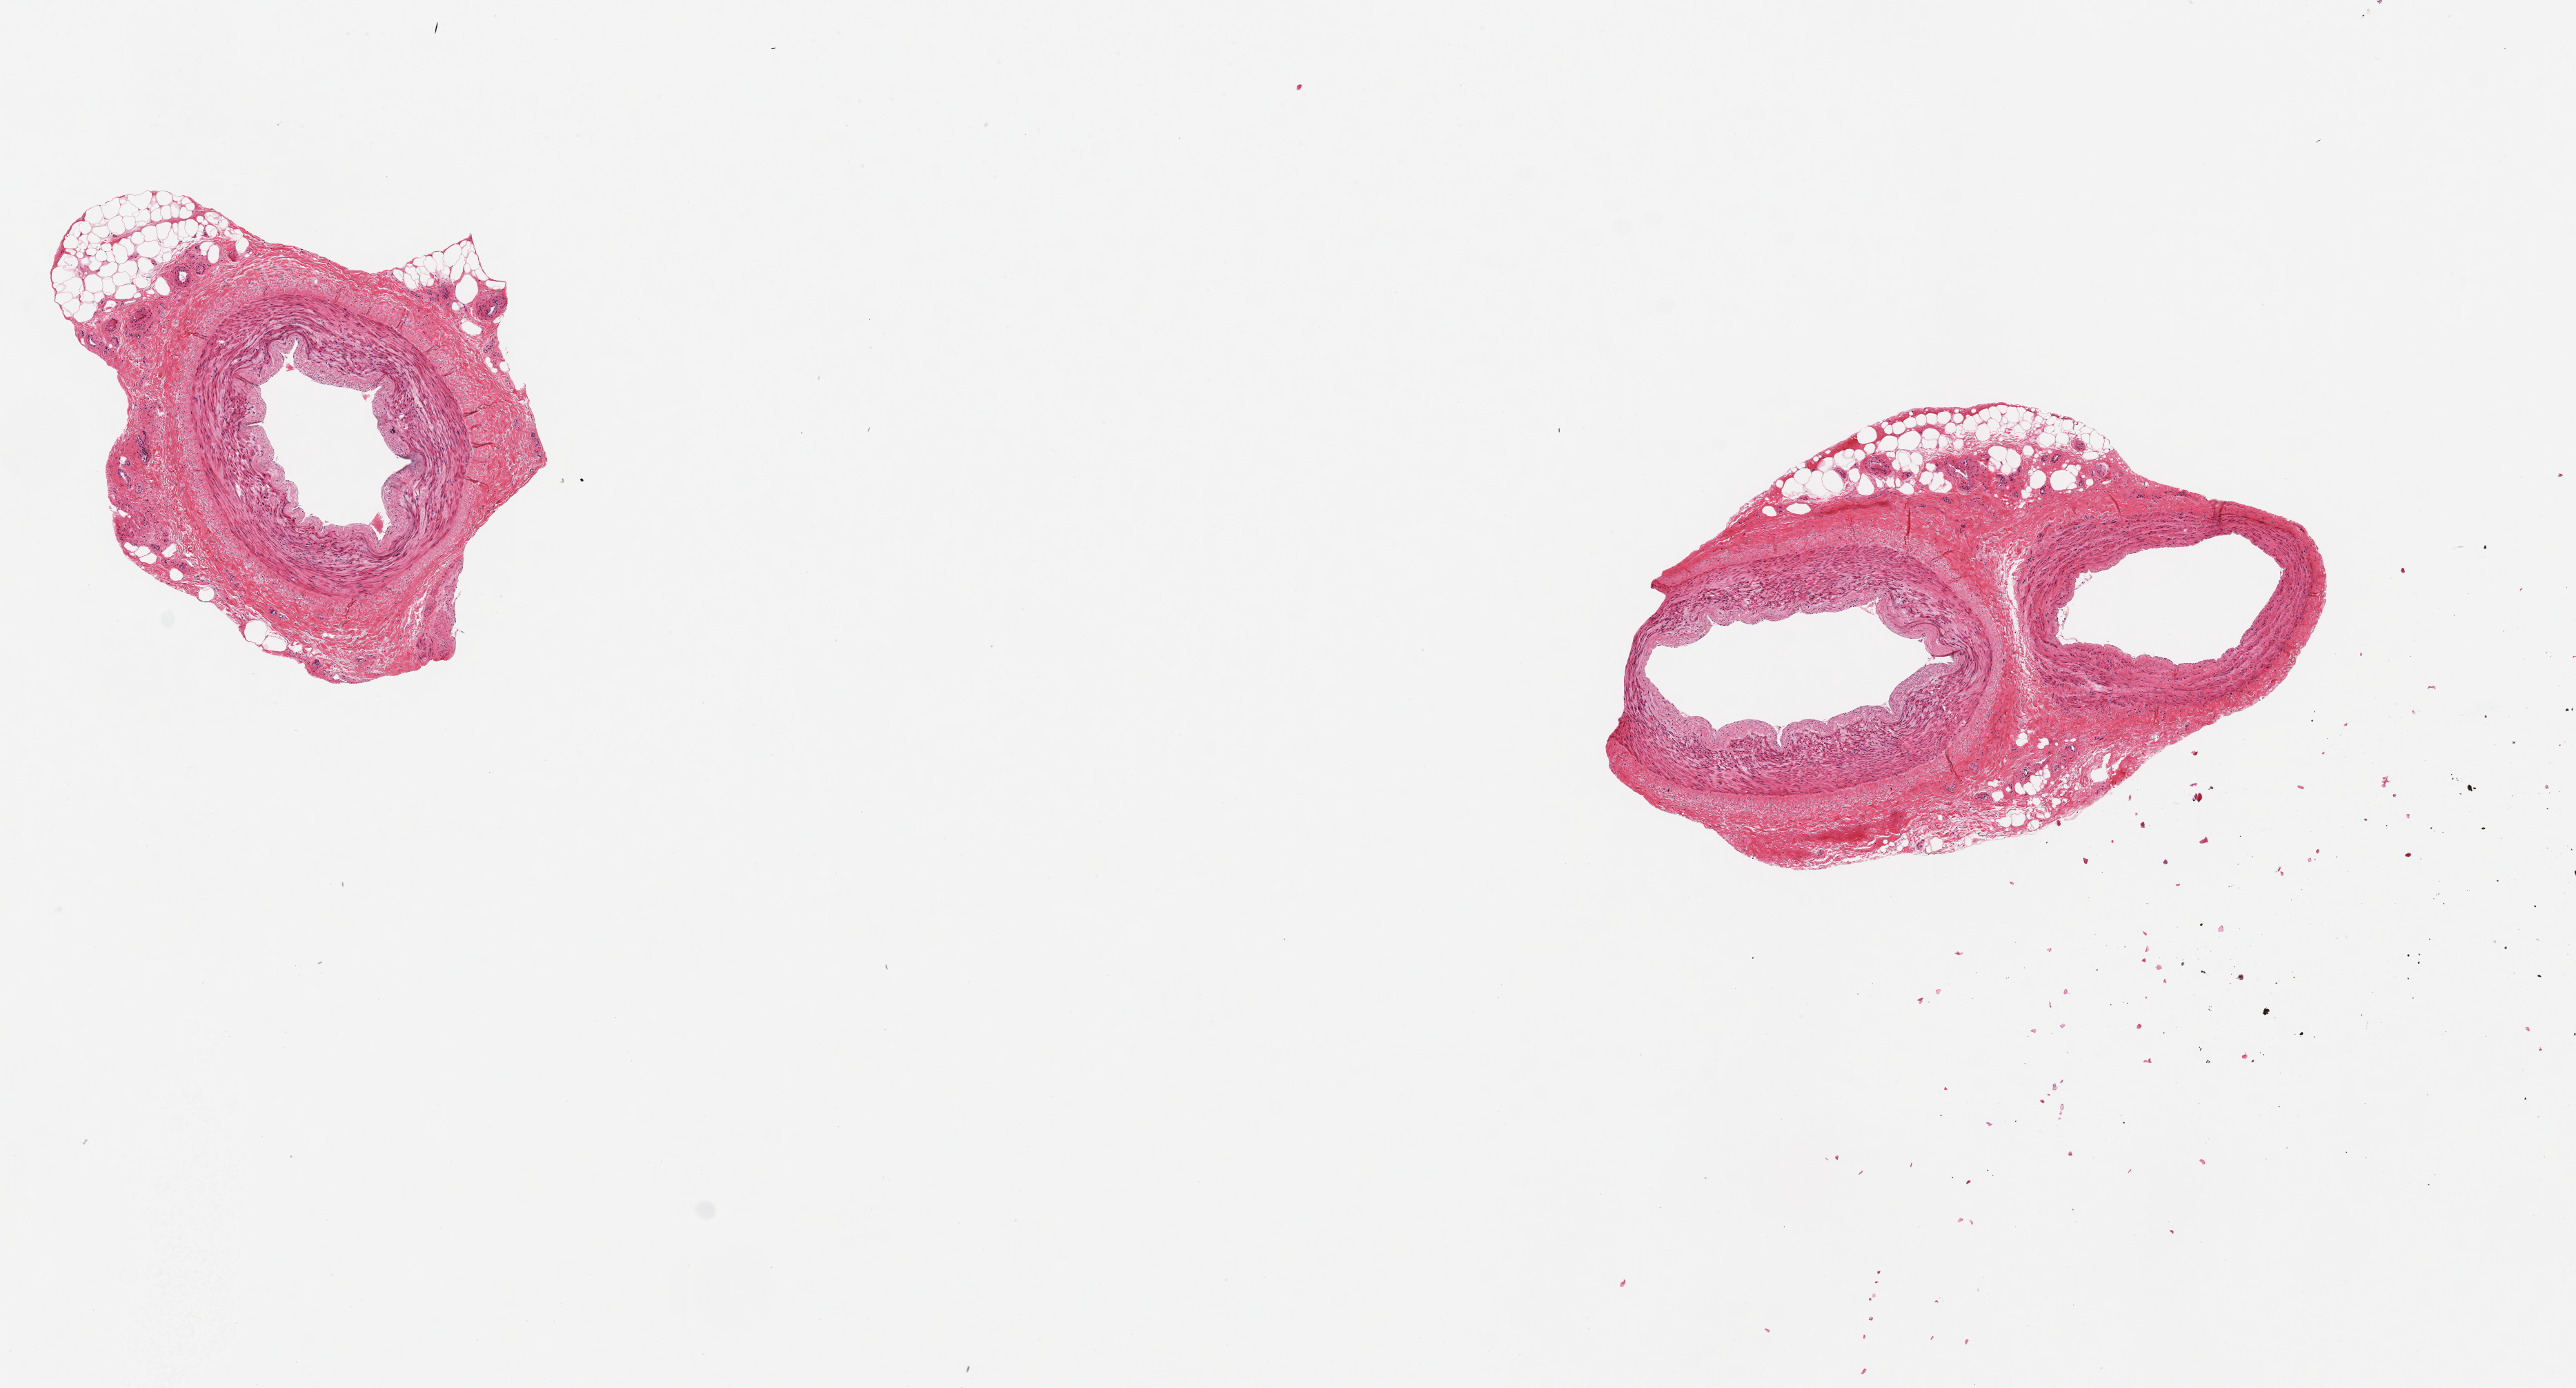
Whole-slide image, H&E stain, whole scanned area (about 14.8 x 8.0 mm) shown as a low-resolution overview; PAXgene-fixed paraffin-embedded (PFPE) section; section of tibial artery (target tissue); tissue donor sample. Donor: male.
Reviewer comment on this tissue sample: 2 pieces, 3x3 & 4x2.5mm; no lesions; 20% peripheral fibroadipose tissue.